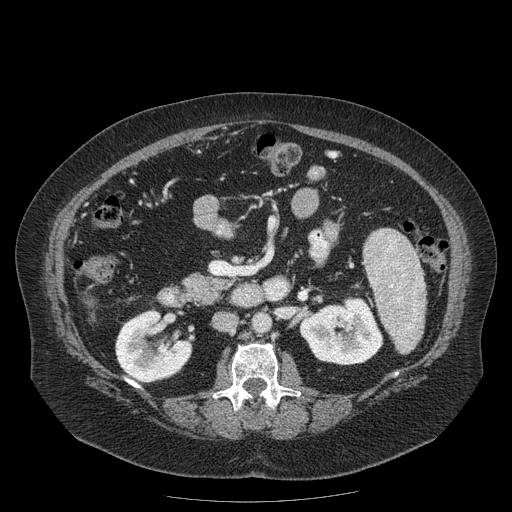
Contrast-enhanced abdominal CT (liver protocol), one axial slice. Slice 49 of 204 in the series (ordered by position). 120 kVp. Soft-tissue window (W 400 / L 40 HU). 2.5 mm slice thickness. 512 × 512 image matrix, field of view 440 × 440 mm. Case-level facts recorded for this patient, not image findings: diagnosis: hepatocellular carcinoma (patient treated with transarterial chemoembolisation; whether this scan precedes or follows treatment is not stated here); TNM stage (as recorded): Stage-IIIB; Child-Pugh class: A; tumour nodularity: uninodular.
Outlined on this slice (semi-automatic segmentation, software-assisted and operator-edited):
- liver parenchyma outside the tumour (the mass and vessels are separate outlines, so this box may not span the whole liver): bounding box <85,300,92,306> (left, top, right, bottom; pixels)